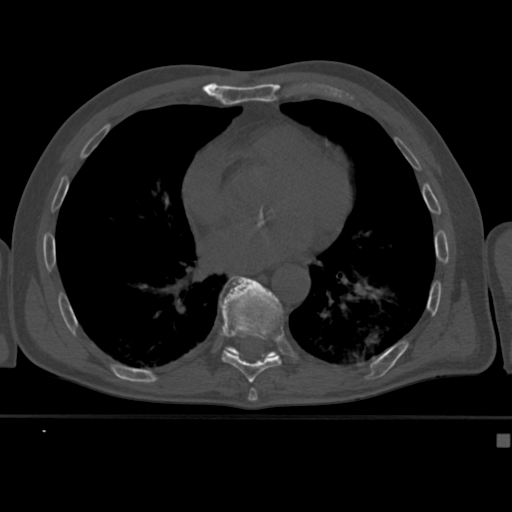
CT including the spine, one axial slice. Position 243 of 430 along the scan axis. Reconstruction kernel Br40s. 120 kVp. Bone window (W 1800 / L 400 HU). 1.5 mm slice thickness. 512 × 512 image matrix, field of view 337 × 337 mm. Male patient, age 64 years. From the clinical record (not read from this slice): primary cancer: uterus.
Structures marked on this image (semi-automatically segmented with operator editing):
- T10 vertebra: bounding box (x1, y1, x2, y2) in pixels: (226, 346, 274, 360)
- T9 vertebra: (219, 276, 283, 382)